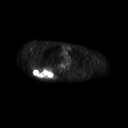
FDG PET of an extremity soft-tissue mass (from a PET/CT study), one axial slice. Position 187 of 267 along the scan axis. 3.27 mm slice thickness. 128 × 128 image matrix, field of view 700 × 700 mm. Patient: male, 61 years. From the clinical record (not read from this slice): histological type: pleiomorphic spindle cell undifferentiated; grade: high; site of the primary tumour: right parascapusular.
Outlined on this slice (expert contour drawn on MRI and transferred to this co-registered scan by the dataset authors):
- gross tumour volume including surrounding oedema: box from (x=32, y=66) to (x=58, y=79) px
- gross tumour volume (mass): (x=33, y=67)–(x=55, y=78)